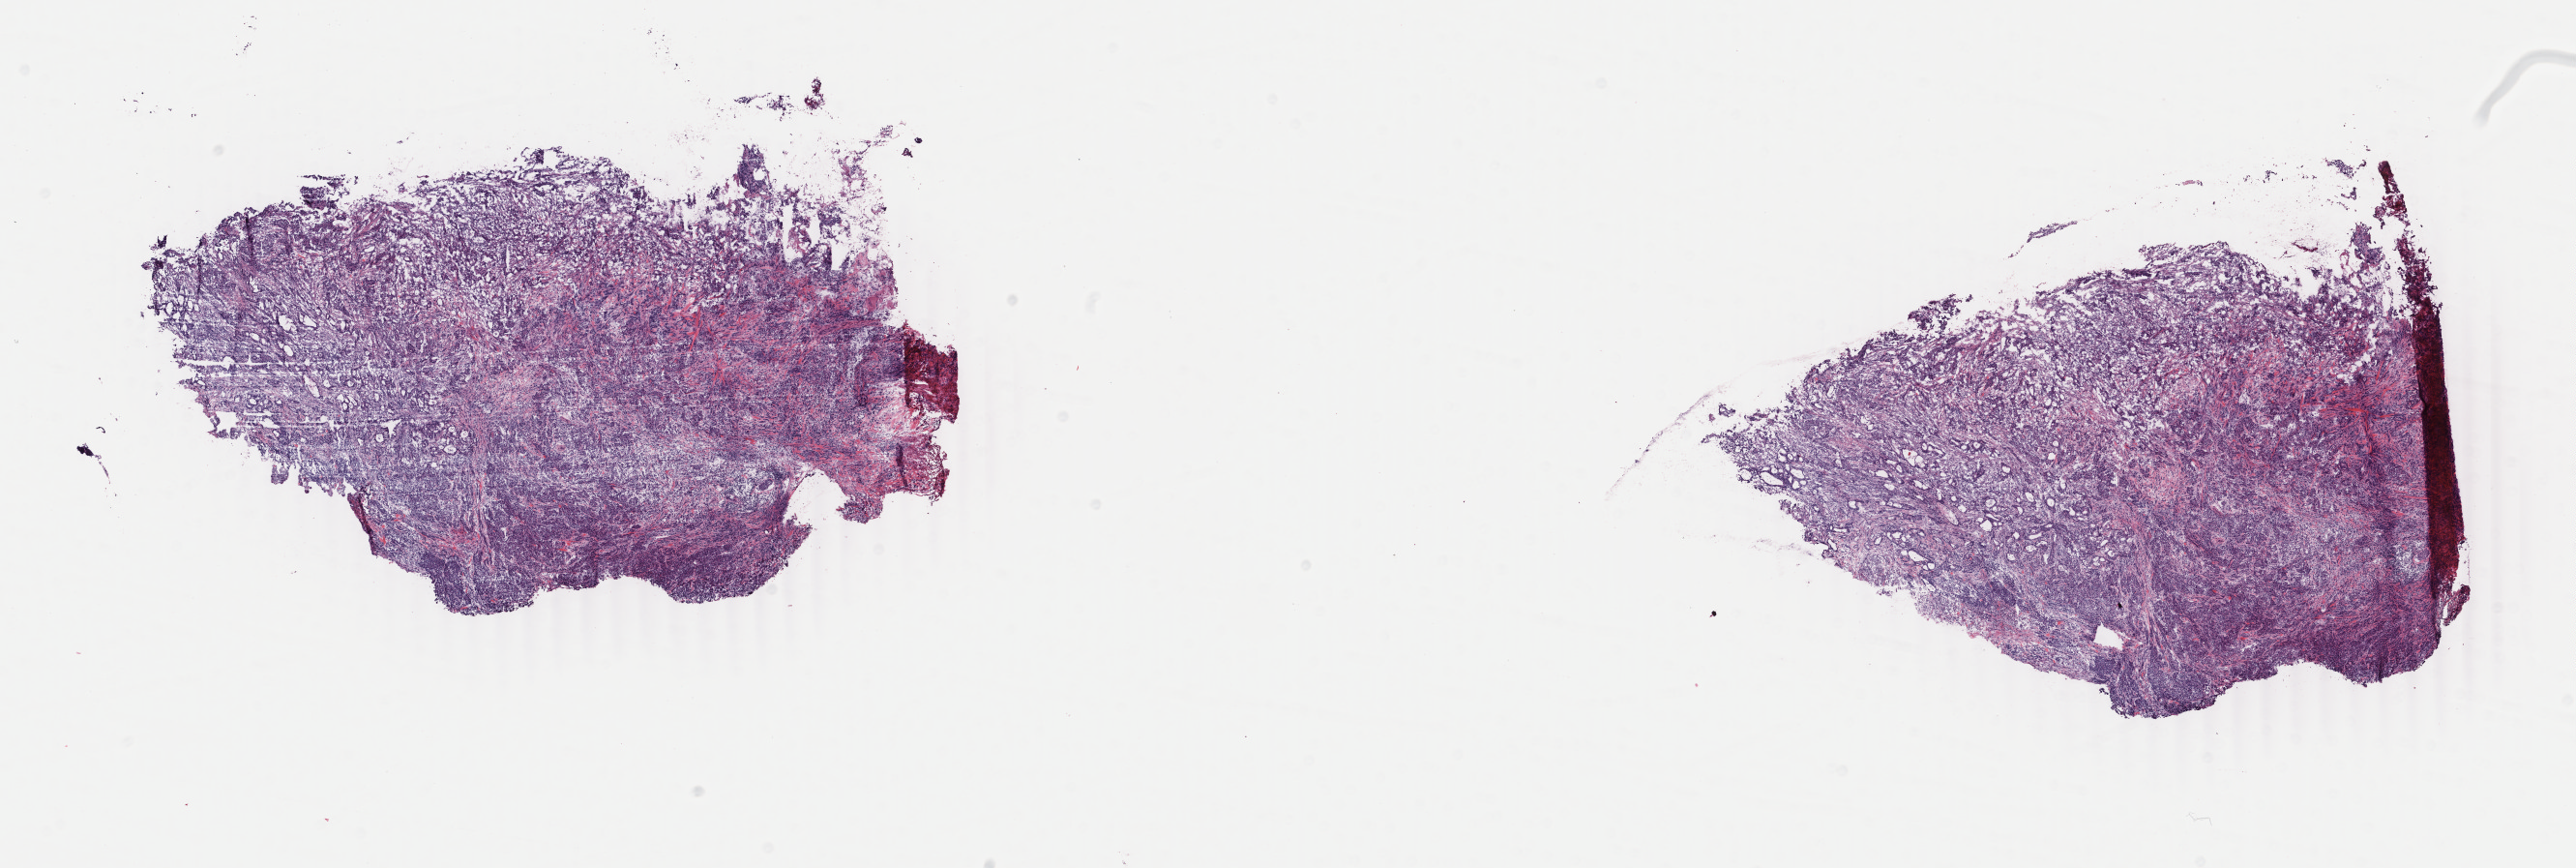
H&E whole-slide image, a low-resolution overview of the entire scanned area, about 21.2 x 7.1 mm (acquisition: 40x scan); frozen section from the bottom of the tissue portion; sample: primary tumour, colon. Female patient; age at initial diagnosis 80 years. Composition of this section per pathologist review: tumour cells 85%, tumour nuclei 85%, normal cells 0%, stromal cells 14%, necrosis 1%. Inflammatory infiltration, as recorded: lymphocyte infiltration 3%, monocyte infiltration 0%, neutrophil infiltration 4%.
* pathologic diagnosis: Adenocarcinoma, NOS (ascending colon)
* TNM: T3 N1 M0
* AJCC pathologic stage: III (5th edition)
* lymph nodes positive (case pathology): 1 of 21 examined